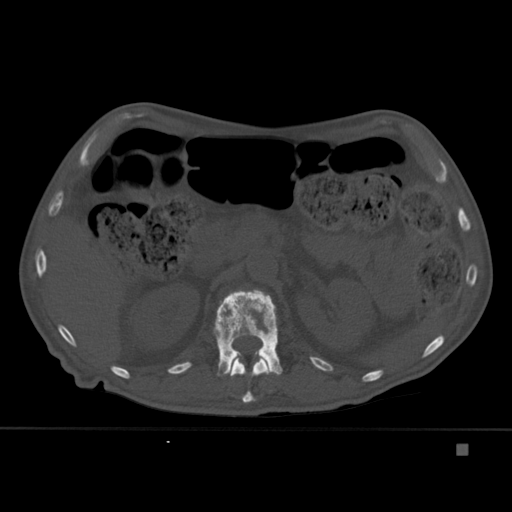
CT including the spine, one axial slice; bone window (W 1800 / L 400 HU); 512 × 512 image matrix, field of view 378 × 378 mm. Male patient, age 75 years. Case-level facts recorded for this patient, not image findings: primary cancer: prostate.
Annotated regions visible in this slice (semi-automatic segmentation, software-assisted and operator-edited):
- L1 vertebra: bounding box [x1, y1, x2, y2] px = [213, 289, 283, 376]
- T12 vertebra: [228, 355, 270, 403]